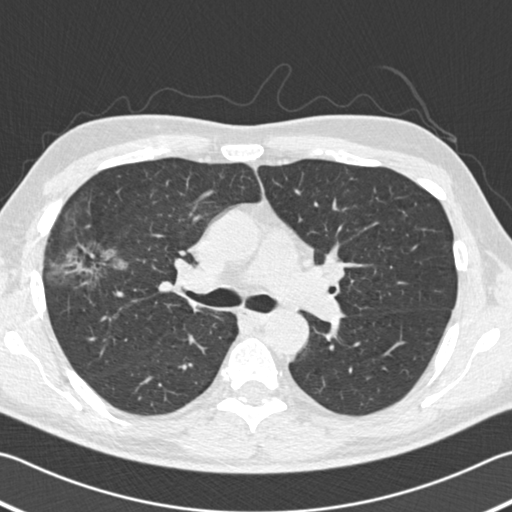
Low-dose screening chest CT, one axial slice. Slice 117 of 182 in the series (ordered by position). Reconstruction kernel B30f. Lung window (W 1500 / L -600 HU). 2 mm slice thickness. 512 × 512 image matrix, field of view 344 × 344 mm.
Annotated regions visible in this slice (outlined manually by an expert reader):
- lesion 1 (tumor, upper lobe of right lung): box from (x=63, y=242) to (x=125, y=279) px